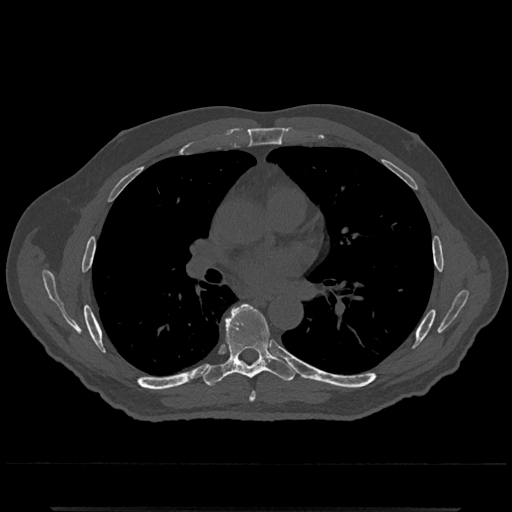
CT including the spine, one axial slice; slice 730 of 797 in the series (ordered by position); 120 kVp; bone window (W 1800 / L 400 HU); 0.5 mm slice thickness; 512 × 512 image matrix, field of view 393 × 393 mm. Patient: male, 67 years. From the clinical record (not read from this slice): primary cancer: prostate.
Annotated regions visible in this slice (semi-automatic segmentation, software-assisted and operator-edited):
- T6 vertebra: bounding box (x1, y1, x2, y2) in pixels: (249, 393, 256, 402)
- T7 vertebra: (204, 304, 297, 386)